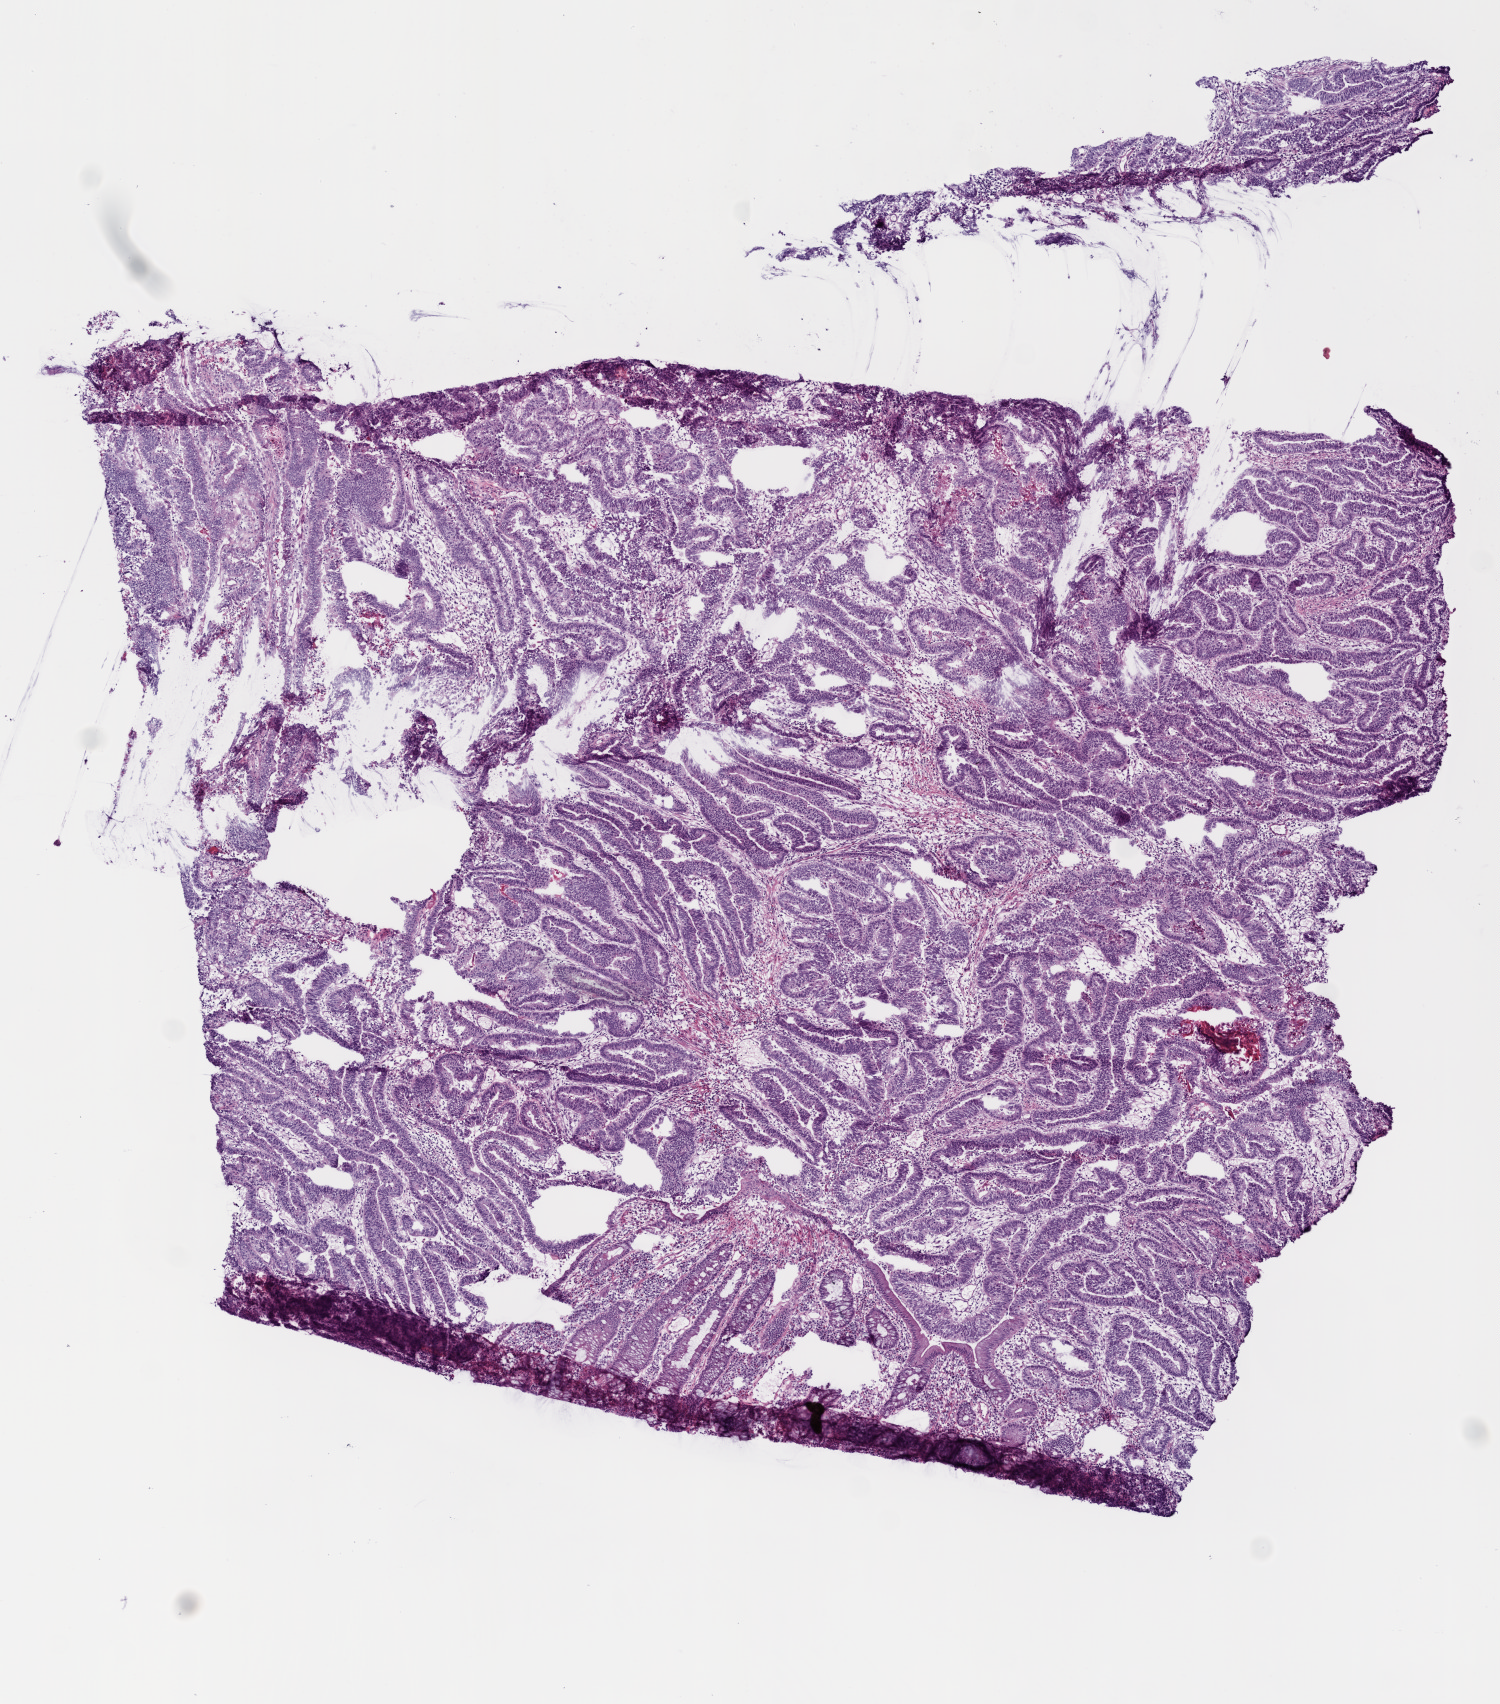
Whole-slide histology image, H&E — low-resolution overview of the scanned area, about 6.0 x 6.8 mm (from a 20x scan). Frozen section from the top of the tissue portion. Sample: primary tumour, rectum. Female, age 67 years at initial diagnosis. Composition of this section per pathologist review: tumour cells 85%, tumour nuclei 80%, normal cells 2%, stromal cells 10%, necrosis 3%.
Pathologic diagnosis: Adenocarcinoma, NOS (rectosigmoid junction). AJCC pathologic stage: I. Lymph nodes positive (case pathology): 0 of 26 examined.